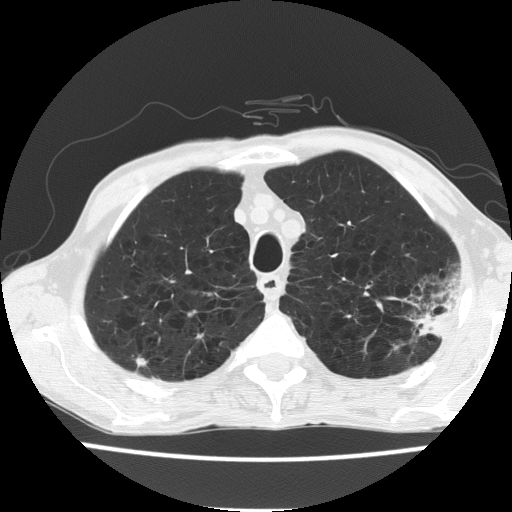
Chest CT (low-dose screening protocol), one axial image. Baseline annual screen. Lung window (W 1500 / L -600 HU). 2 mm slice thickness. Lung (sharp) reconstruction kernel (FC51). 512 × 512 image matrix. Male participant, aged 60 years at enrolment.
• Expert-annotated lung lesion, bounding box <394,276,463,346> (left, top, right, bottom; pixels).
• No non-calcified nodule or mass ≥4 mm was recorded by the screening reader at this exam.
• Official screen result: negative screen, minor abnormalities not suspicious for lung cancer.
• Later outcome: lung cancer diagnosed 490 days after this screen (after the second annual screen) — bronchiolo-alveolar carcinoma, mucinous, left upper lobe, stage IV (AJCC 6th edition).